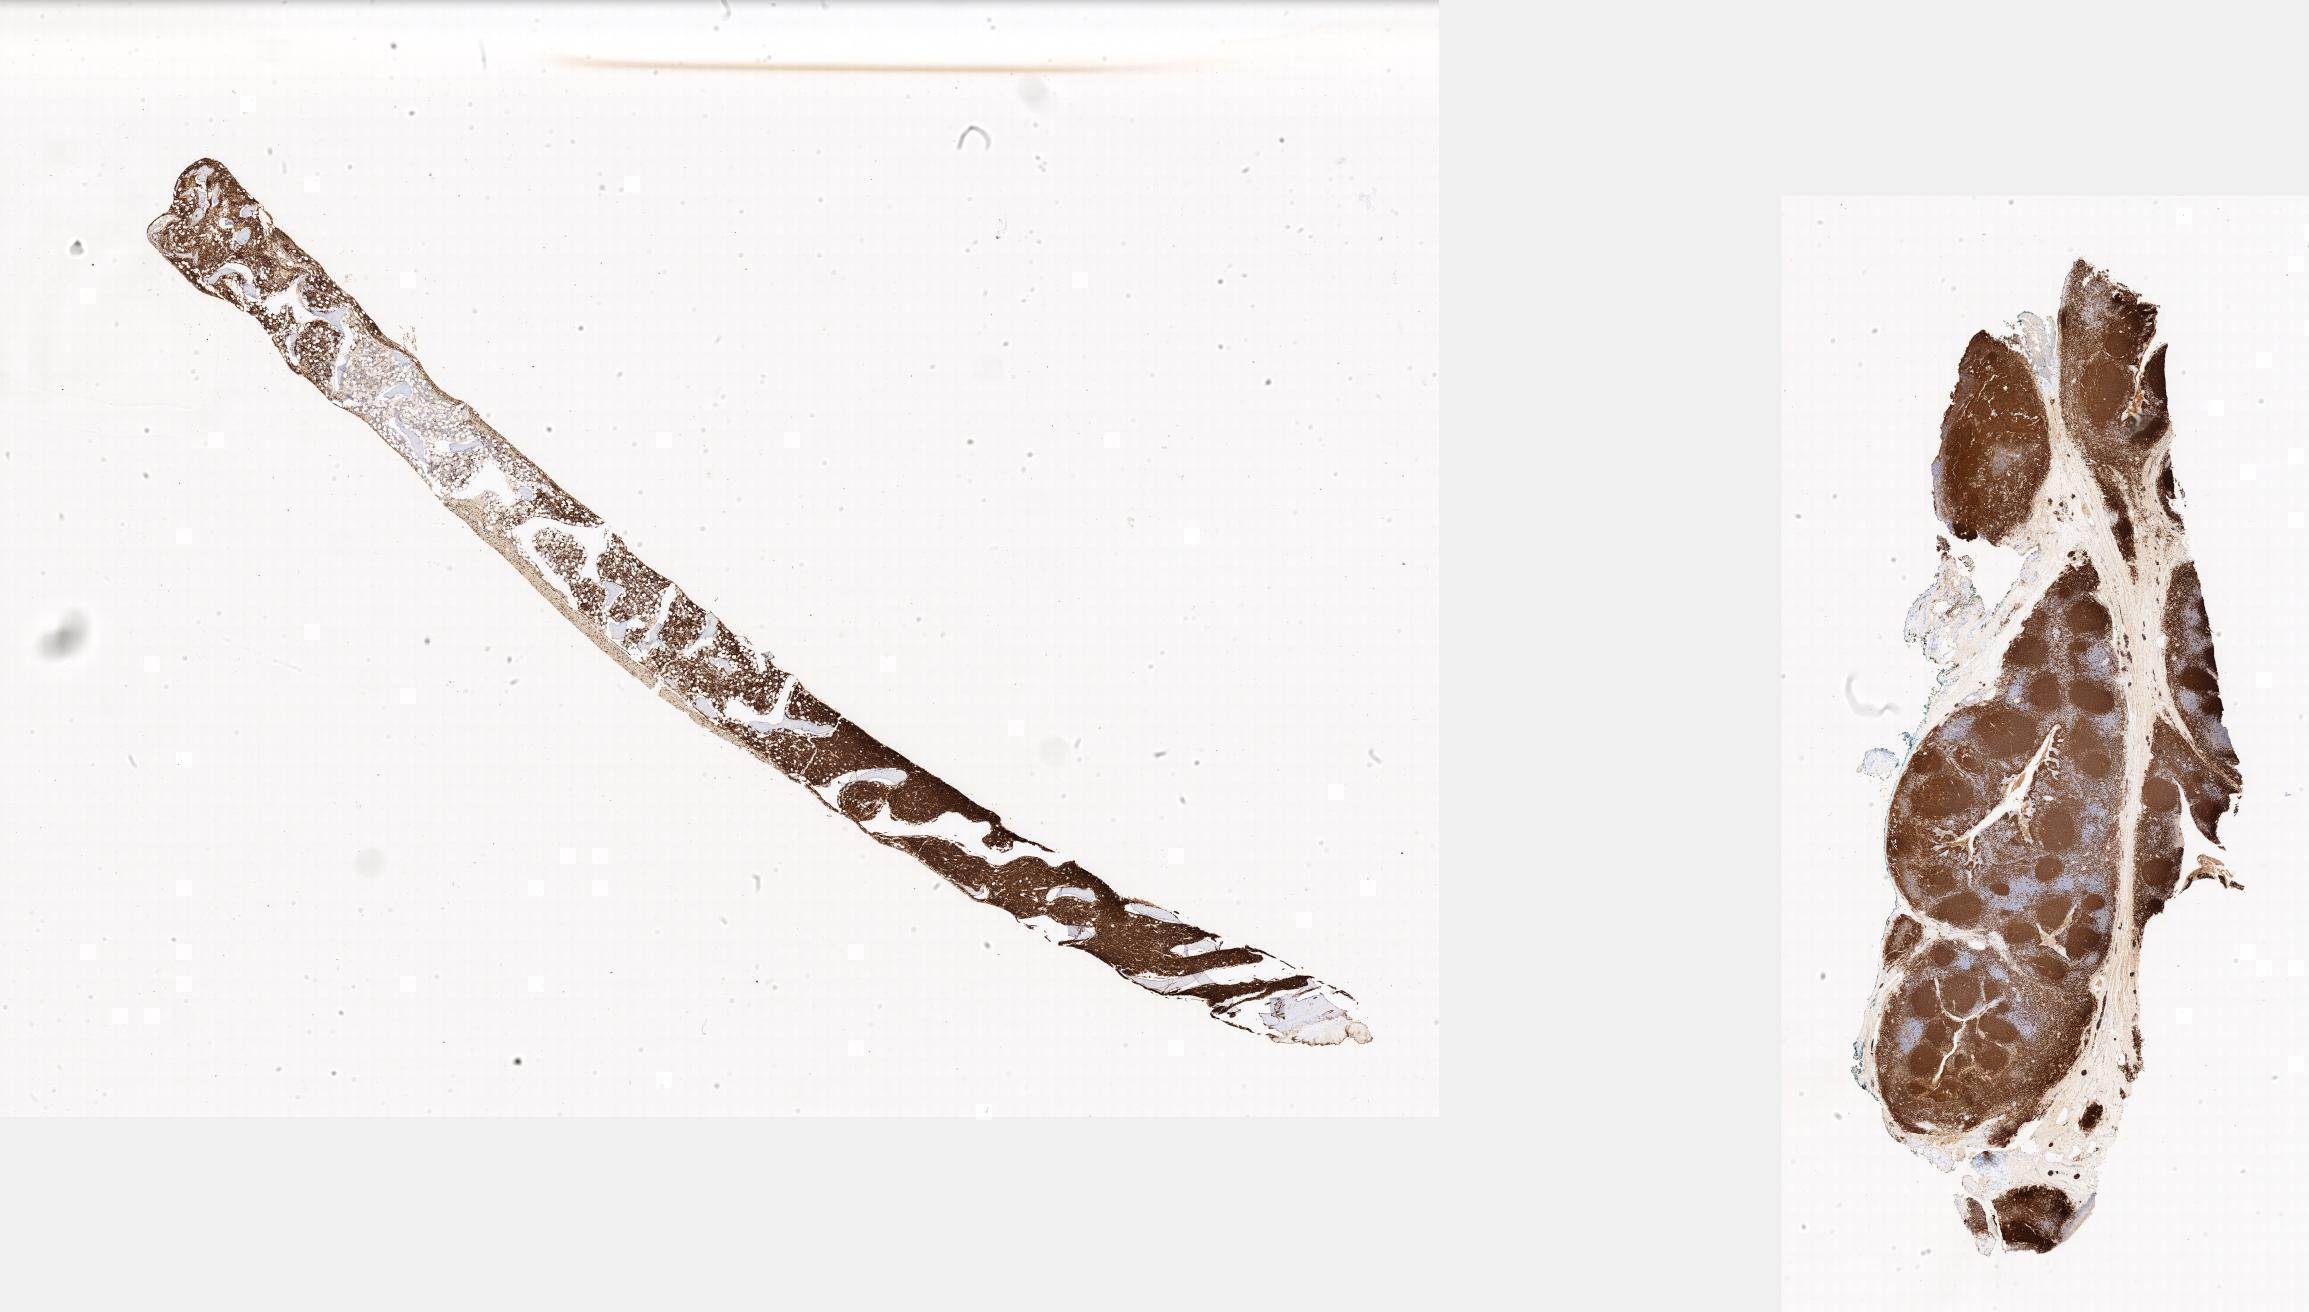
IHC for CD20, whole-slide image, a low-resolution overview of the entire scanned area; specimen: tumor tissue. Patient: male, 12 years old.
Histologic diagnosis: Burkitt lymphoma, NOS.